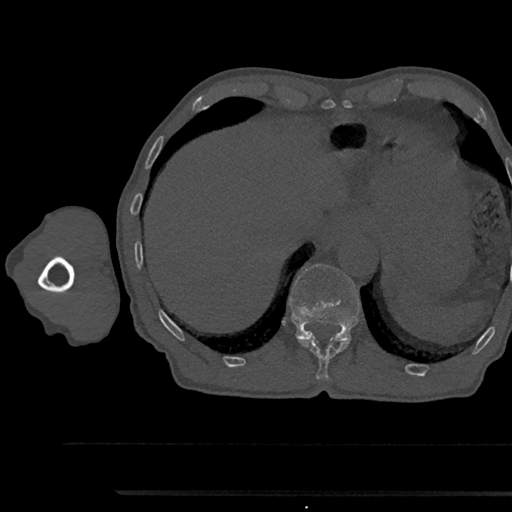
CT including the spine, one axial slice. Slice 750 of 797 in the series (ordered by position). Bone window (W 1800 / L 400 HU). 512 × 512 image matrix, field of view 367 × 367 mm. Male patient, age 79 years. Case-level facts recorded for this patient, not image findings: primary cancer: prostate.
Annotated regions visible in this slice (semi-automatic segmentation, software-assisted and operator-edited):
- T11 vertebra: bounding box [x1, y1, x2, y2] px = [300, 340, 348, 379]
- T12 vertebra: [289, 264, 360, 342]